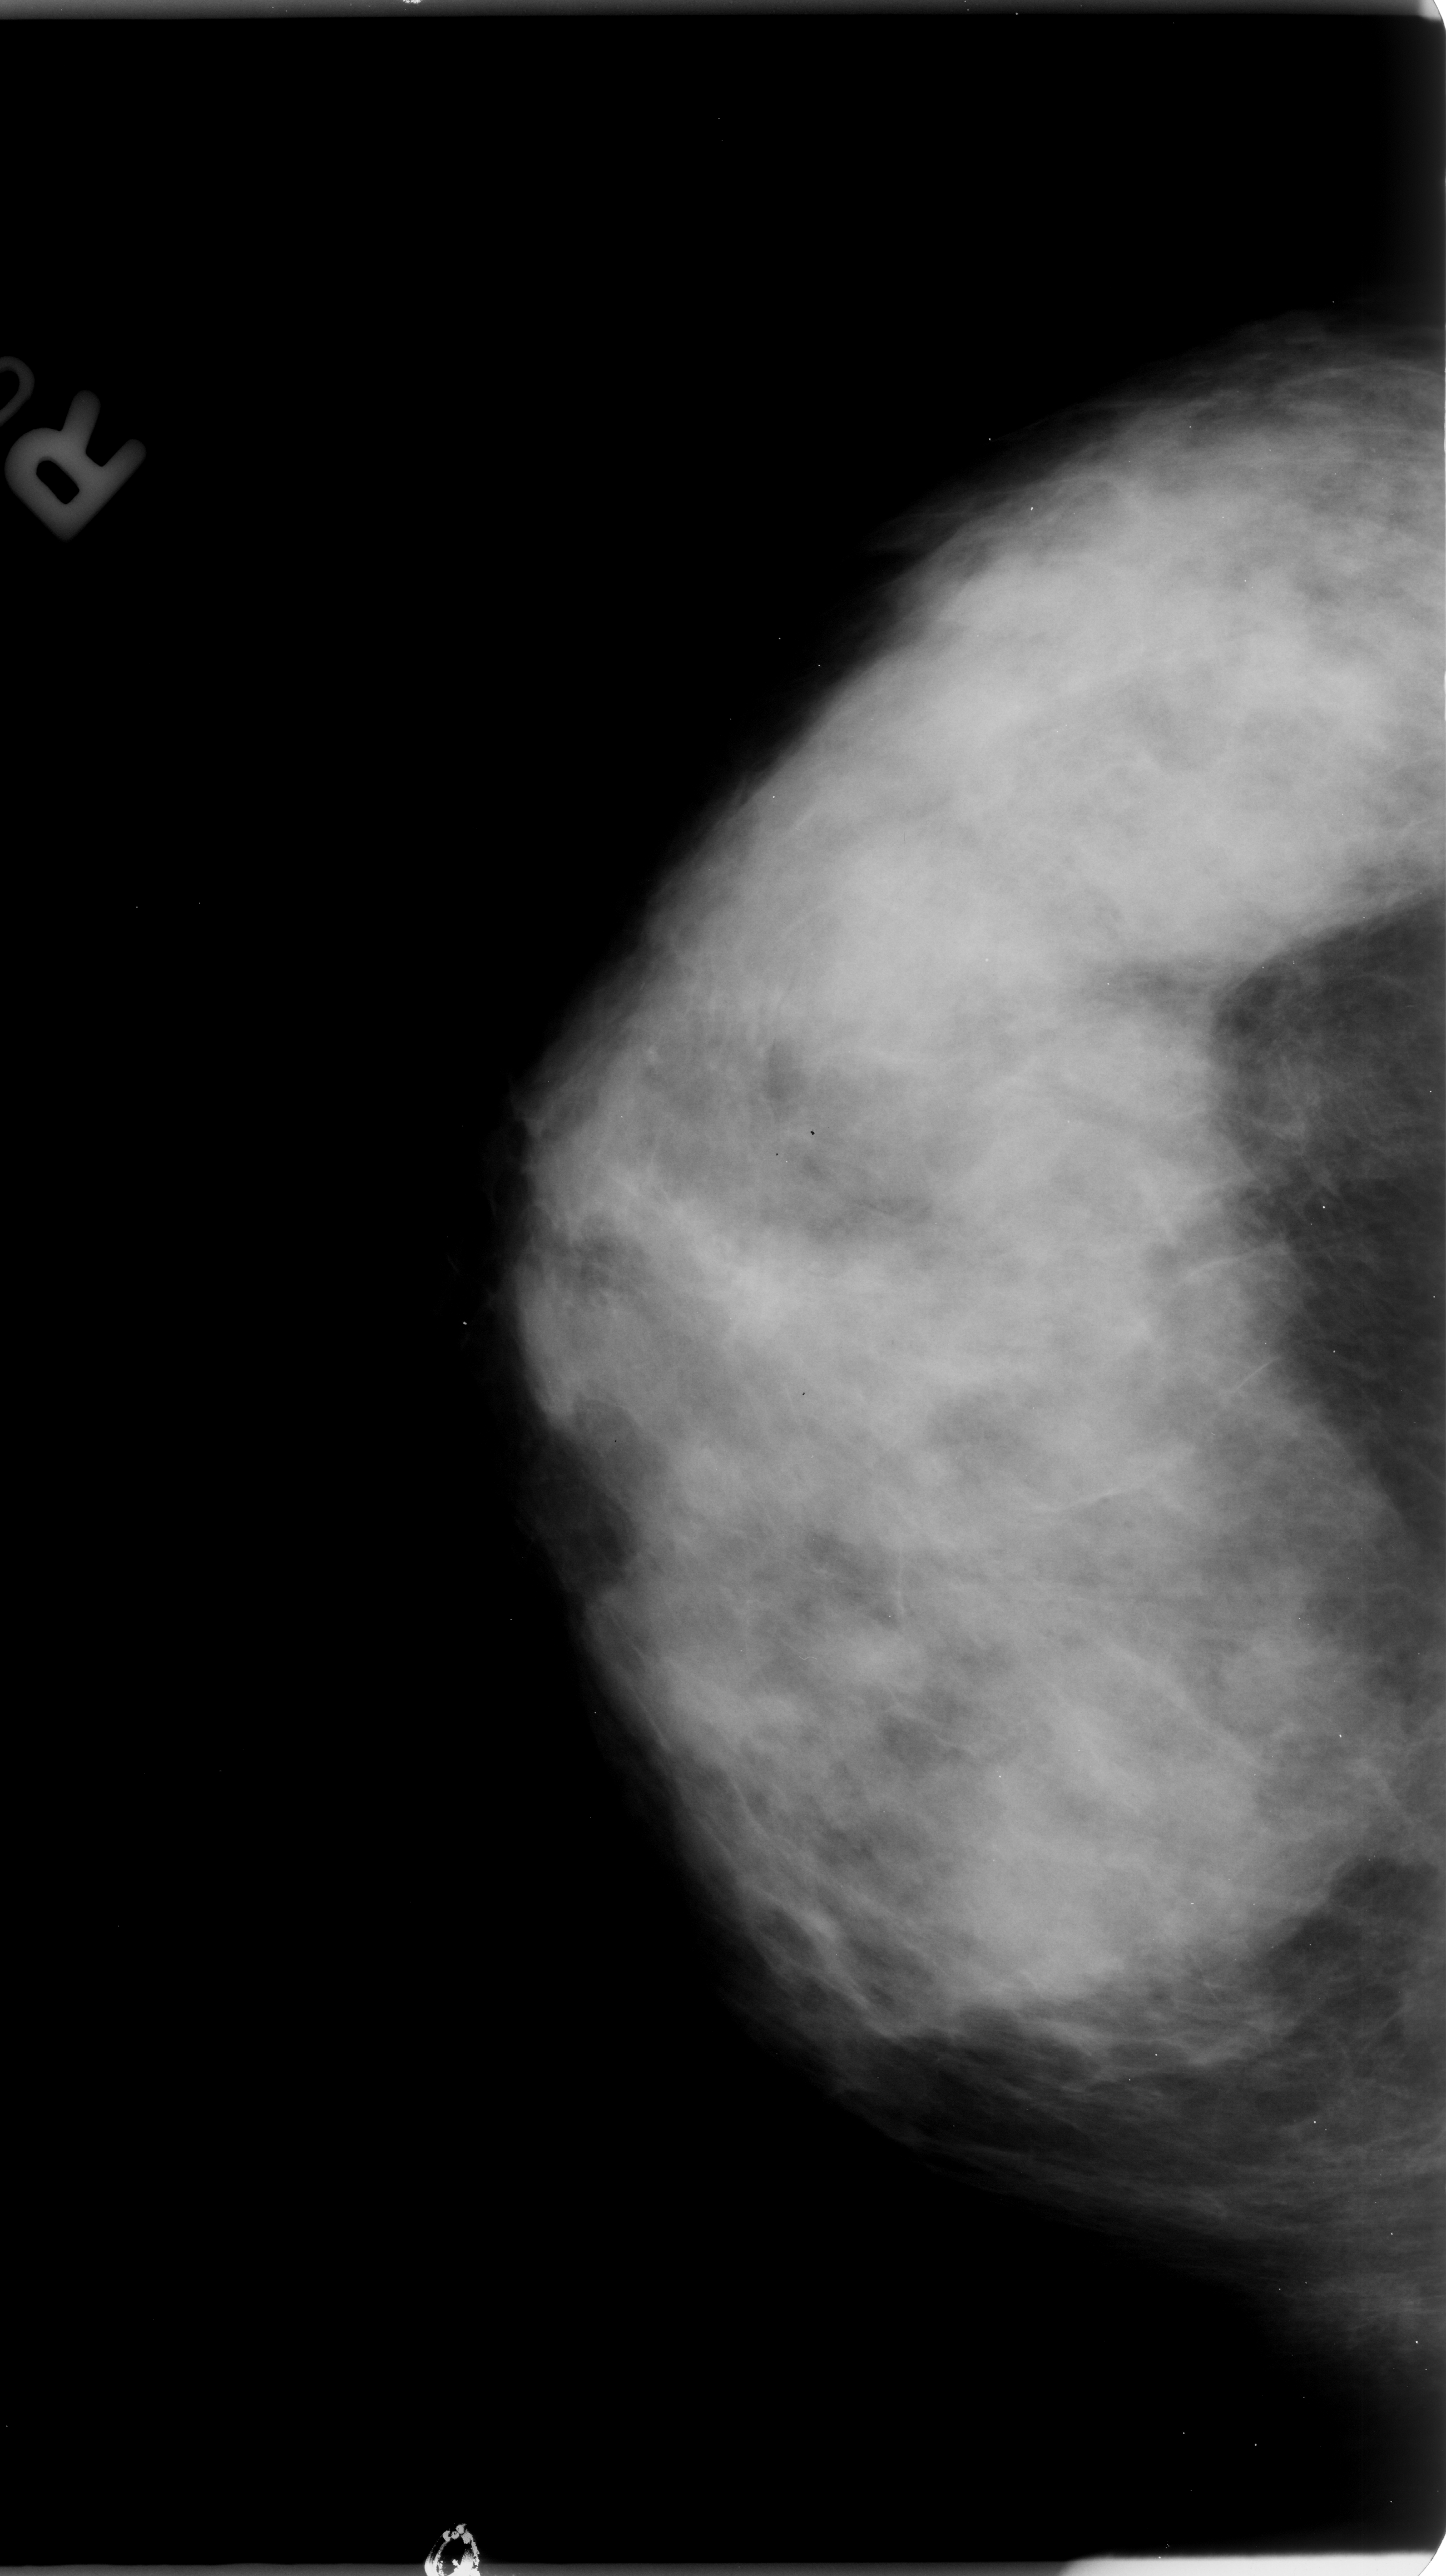
Mammogram (digitized film). Right breast. Craniocaudal (CC) view. Breast composition: extremely dense (BI-RADS density category 4 of 4). 1446 × 2576 image matrix.
Expert-marked regions of interest on this image (one box per marked abnormality):
- mass, shape round, margins circumscribed / obscured; BI-RADS assessment category 3; subtlety rating 2 on a 1 (subtle) to 5 (obvious) scale; pathology result (as recorded, not read from the image): benign: bounding box (x1, y1, x2, y2) in pixels: (781, 832, 954, 1050)